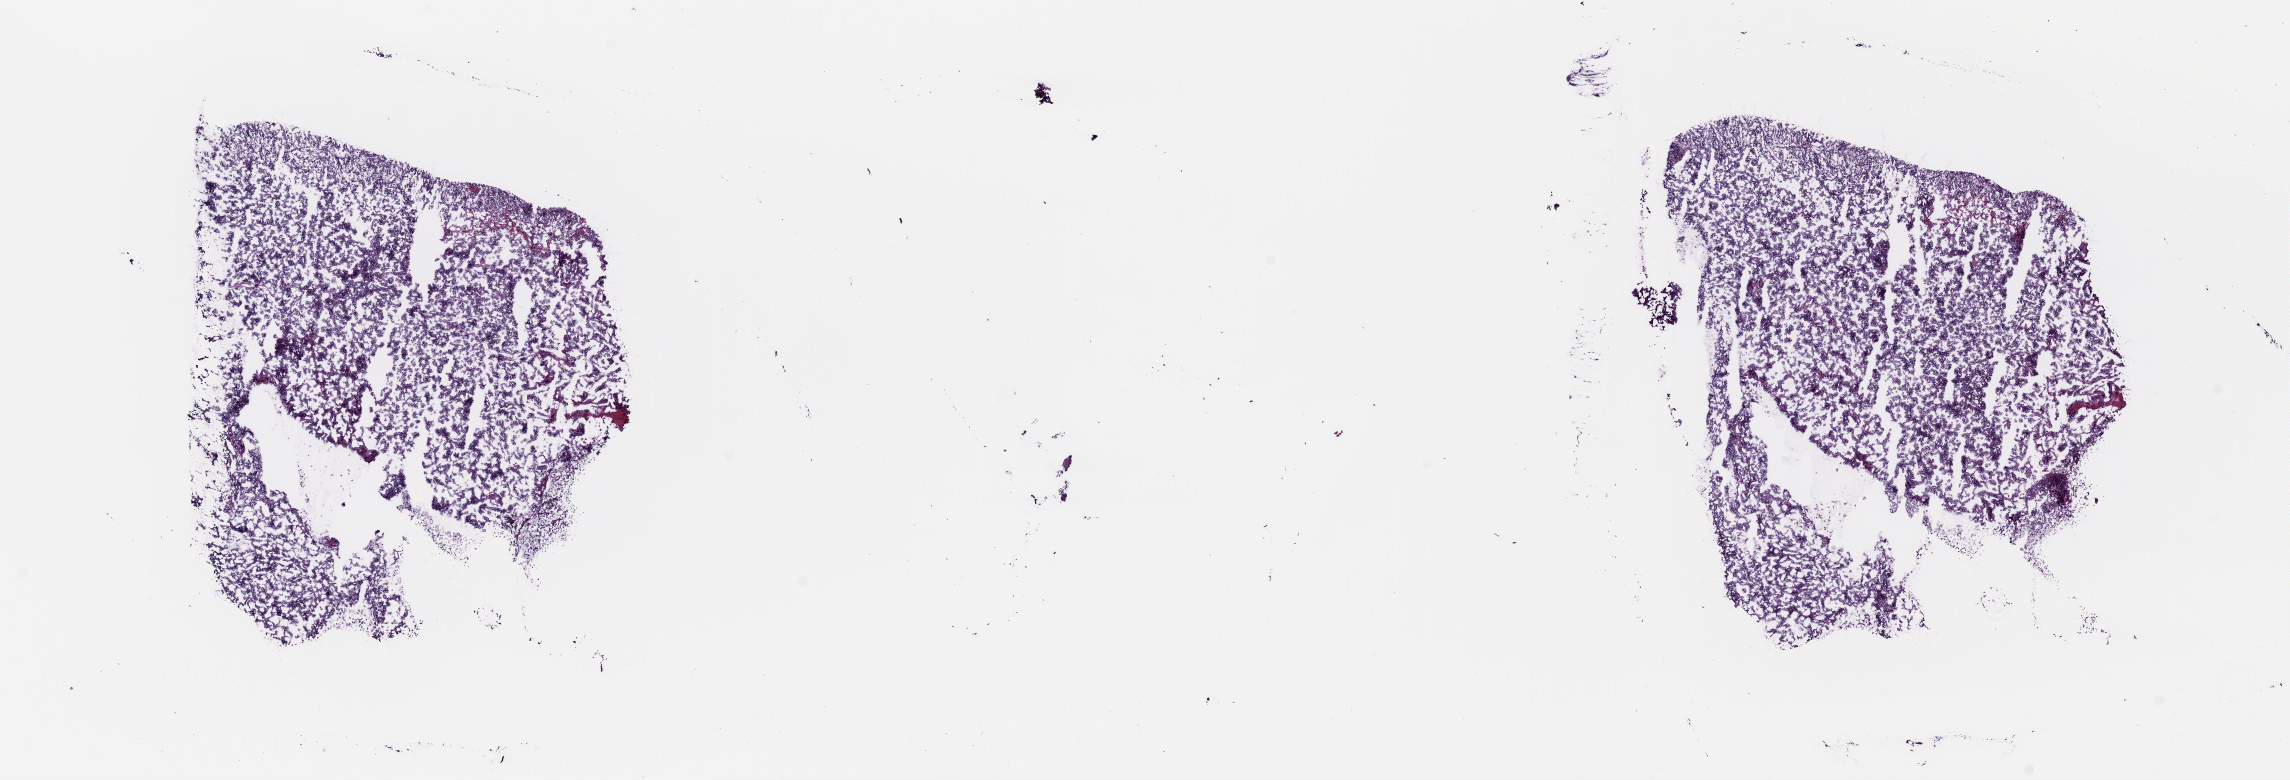
H&E-stained whole-slide image — shown as a low-resolution overview of the whole scanned area (about 18.1 x 6.2 mm). Frozen section from the top of the tissue portion. Uterus, primary tumour sample. Female, age 53 years at initial diagnosis. Histologic grade: G3 (poorly differentiated). Pathologist review of this section (percent, as recorded): tumour cells 94%, tumour nuclei 98%, normal cells 0%, stromal cells 3%, necrosis 3%. Inflammatory infiltration, as recorded: lymphocyte infiltration 0%, monocyte infiltration 0%, neutrophil infiltration 0%.
FIGO stage: IIIC. Histologic diagnosis: Endometrioid adenocarcinoma, NOS (endometrium).